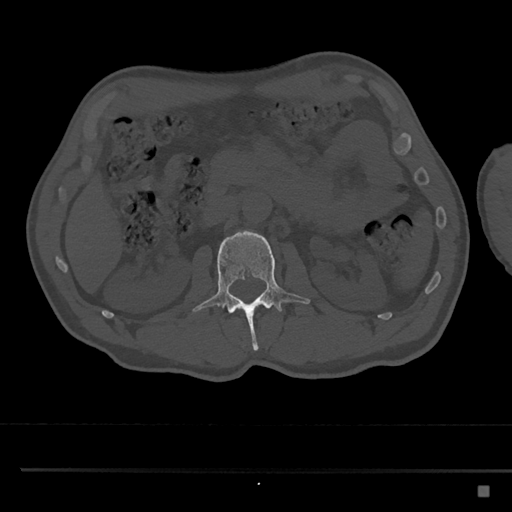
CT including the spine, one axial slice; position 764 of 797 along the scan axis; reconstruction kernel Br40s/3; bone window (W 1800 / L 400 HU); 0.5 mm slice thickness; 512 × 512 image matrix. Male patient, age 59 years. Case-level facts recorded for this patient, not image findings: primary cancer: prostate.
Outlined on this slice (semi-automatically segmented with operator editing):
- L2 vertebra: bounding box [x1, y1, x2, y2] px = [192, 230, 310, 352]